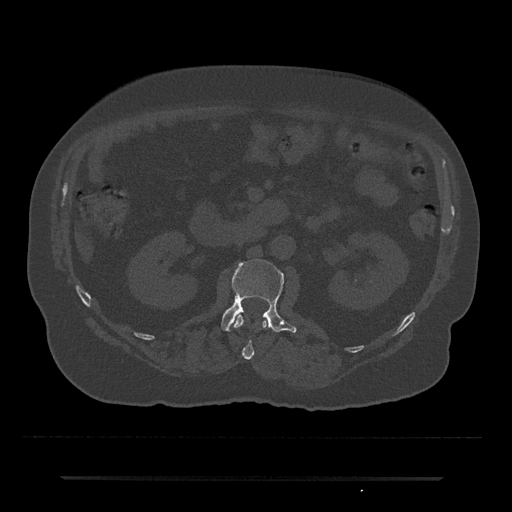
CT including the spine, one axial slice. Slice 28 of 797 in the series (ordered by position). Bone window (W 1800 / L 400 HU). 512 × 512 image matrix, field of view 437 × 437 mm. Patient: male, 69 years. From the clinical record (not read from this slice): primary cancer: prostate.
Annotated regions visible in this slice (semi-automatic segmentation, software-assisted and operator-edited):
- L1 vertebra: bounding box (x1, y1, x2, y2) in pixels: (234, 314, 267, 360)
- L2 vertebra: (221, 259, 297, 333)